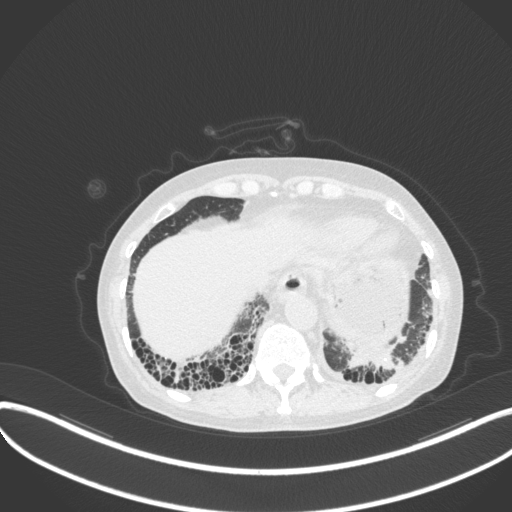
Chest CT, one axial slice; position 56 of 373 along the scan axis; reconstruction kernel B31f; 120 kVp; lung window (W 1500 / L -600 HU); 1 mm slice thickness; 512 × 512 image matrix, field of view 400 × 400 mm. Female patient, age 56 years. Case-level facts recorded for this patient, not image findings: clinical TNM (as recorded): T1 N0 M0.
Annotated regions visible in this slice (rectangle marked by the reading radiologist):
- lung tumour (recorded histology: adenocarcinoma): bounding box <340,342,405,380> (left, top, right, bottom; pixels)